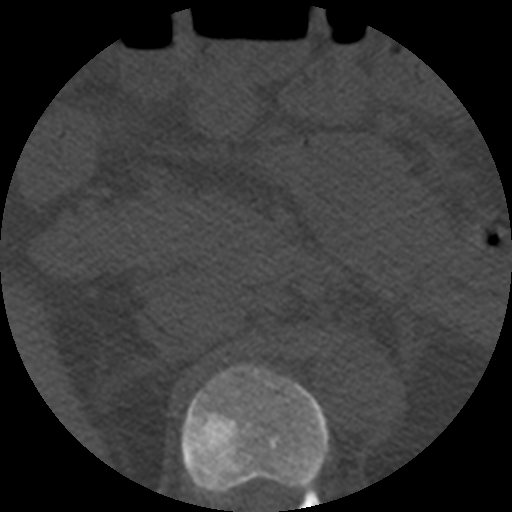
CT including the spine, one axial slice. Slice 225 of 508 in the series (ordered by position). Bone window (W 1800 / L 400 HU). 1.25 mm slice thickness. 512 × 512 image matrix, field of view 160 × 160 mm. Patient age 57 years. Case-level facts recorded for this patient, not image findings: primary cancer: prostate.
Outlined on this slice (semi-automatic segmentation, software-assisted and operator-edited):
- T12 vertebra: bounding box (x1, y1, x2, y2) in pixels: (181, 364, 329, 512)